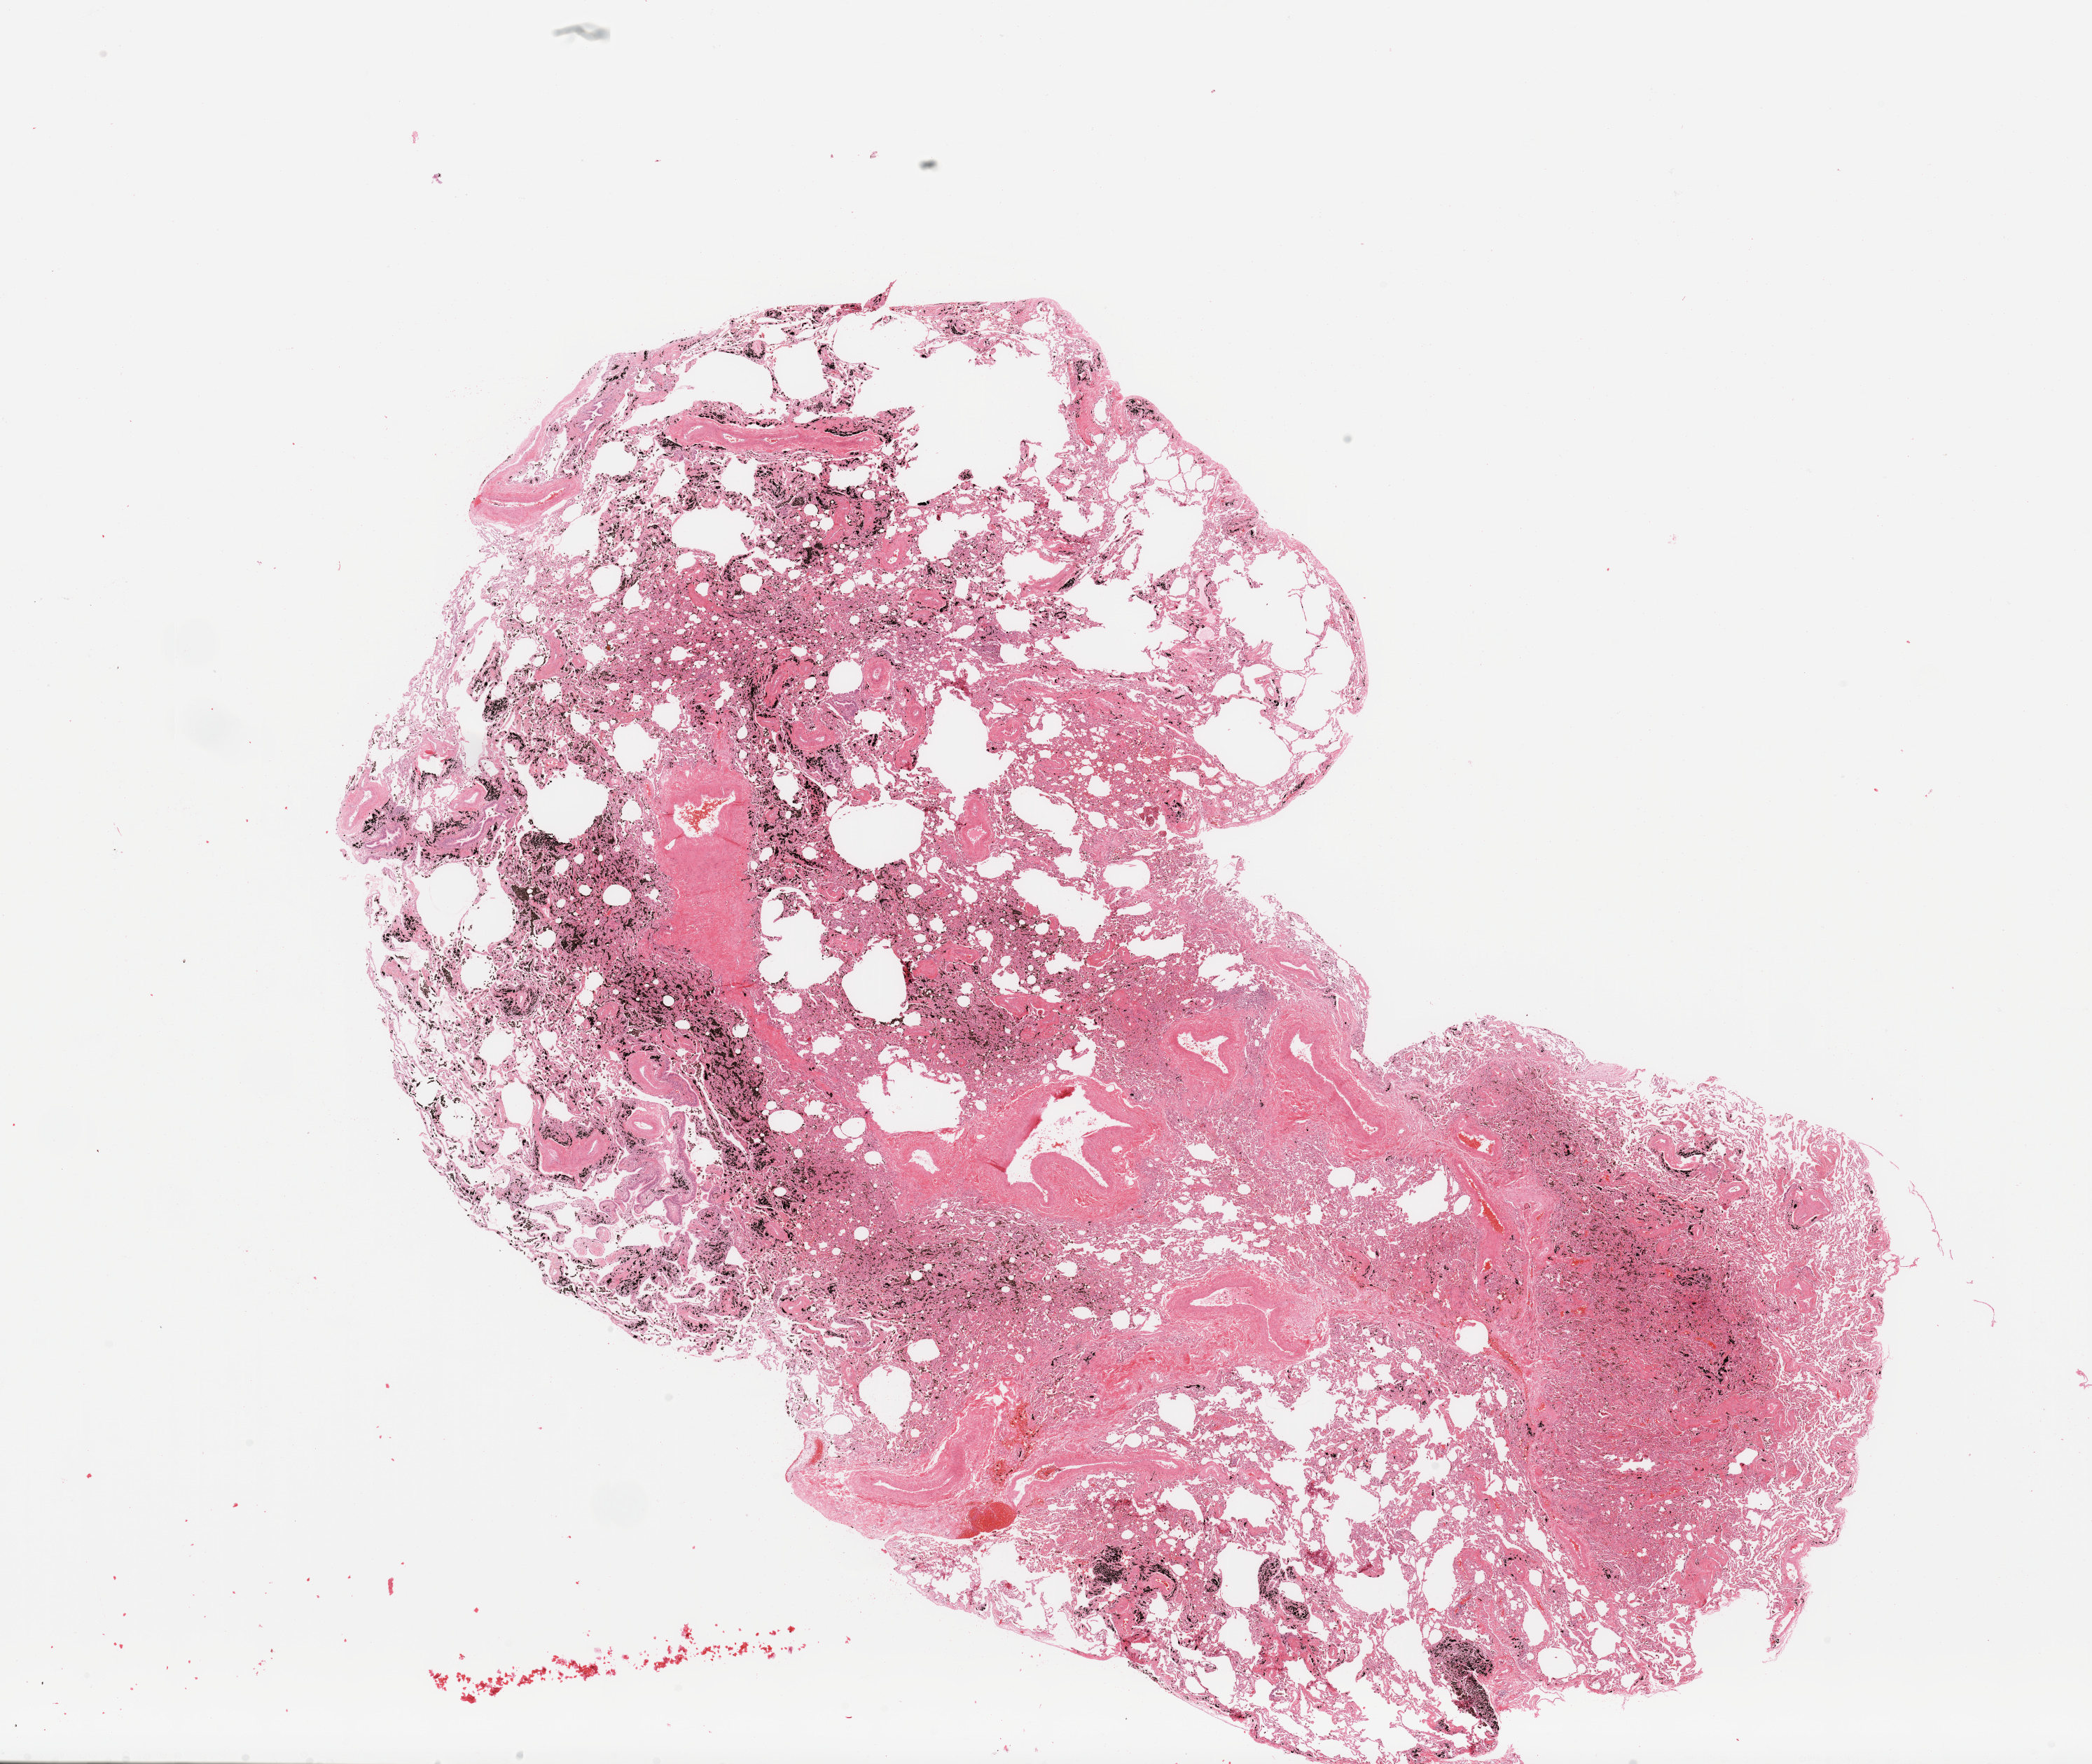
Whole-slide histology image, H&E — low-resolution overview of the scanned area, about 23.6 x 19.9 mm (acquisition: 20x scan). Lung, normal (non-tumour) tissue. 56-year-old male patient.
This section: normal (non-tumour) tissue from the same patient. Patient diagnosis: Squamous cell carcinoma, NOS.